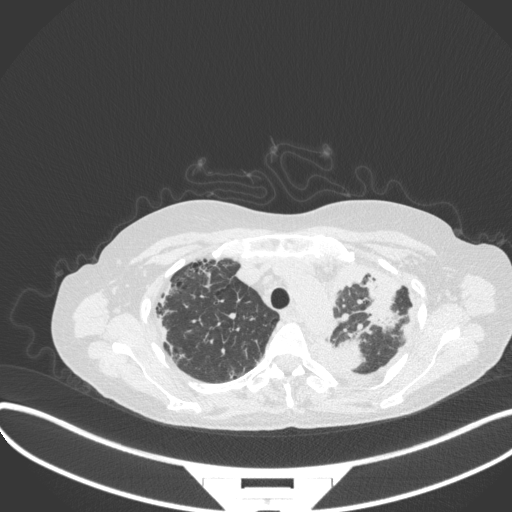
Chest CT, one axial slice. Slice 269 of 373 in the series (ordered by position). 120 kVp. Lung window (W 1500 / L -600 HU). 1 mm slice thickness. 512 × 512 image matrix, field of view 400 × 400 mm. Patient: female, 56 years. Case-level facts recorded for this patient, not image findings: clinical TNM (as recorded): T1 N0 M0.
Annotated regions visible in this slice (bounding box drawn by a radiologist):
- lung tumour (recorded histology: adenocarcinoma): box from (x=334, y=334) to (x=367, y=375) px
- lung tumour (recorded histology: adenocarcinoma): (x=361, y=273)–(x=402, y=332)